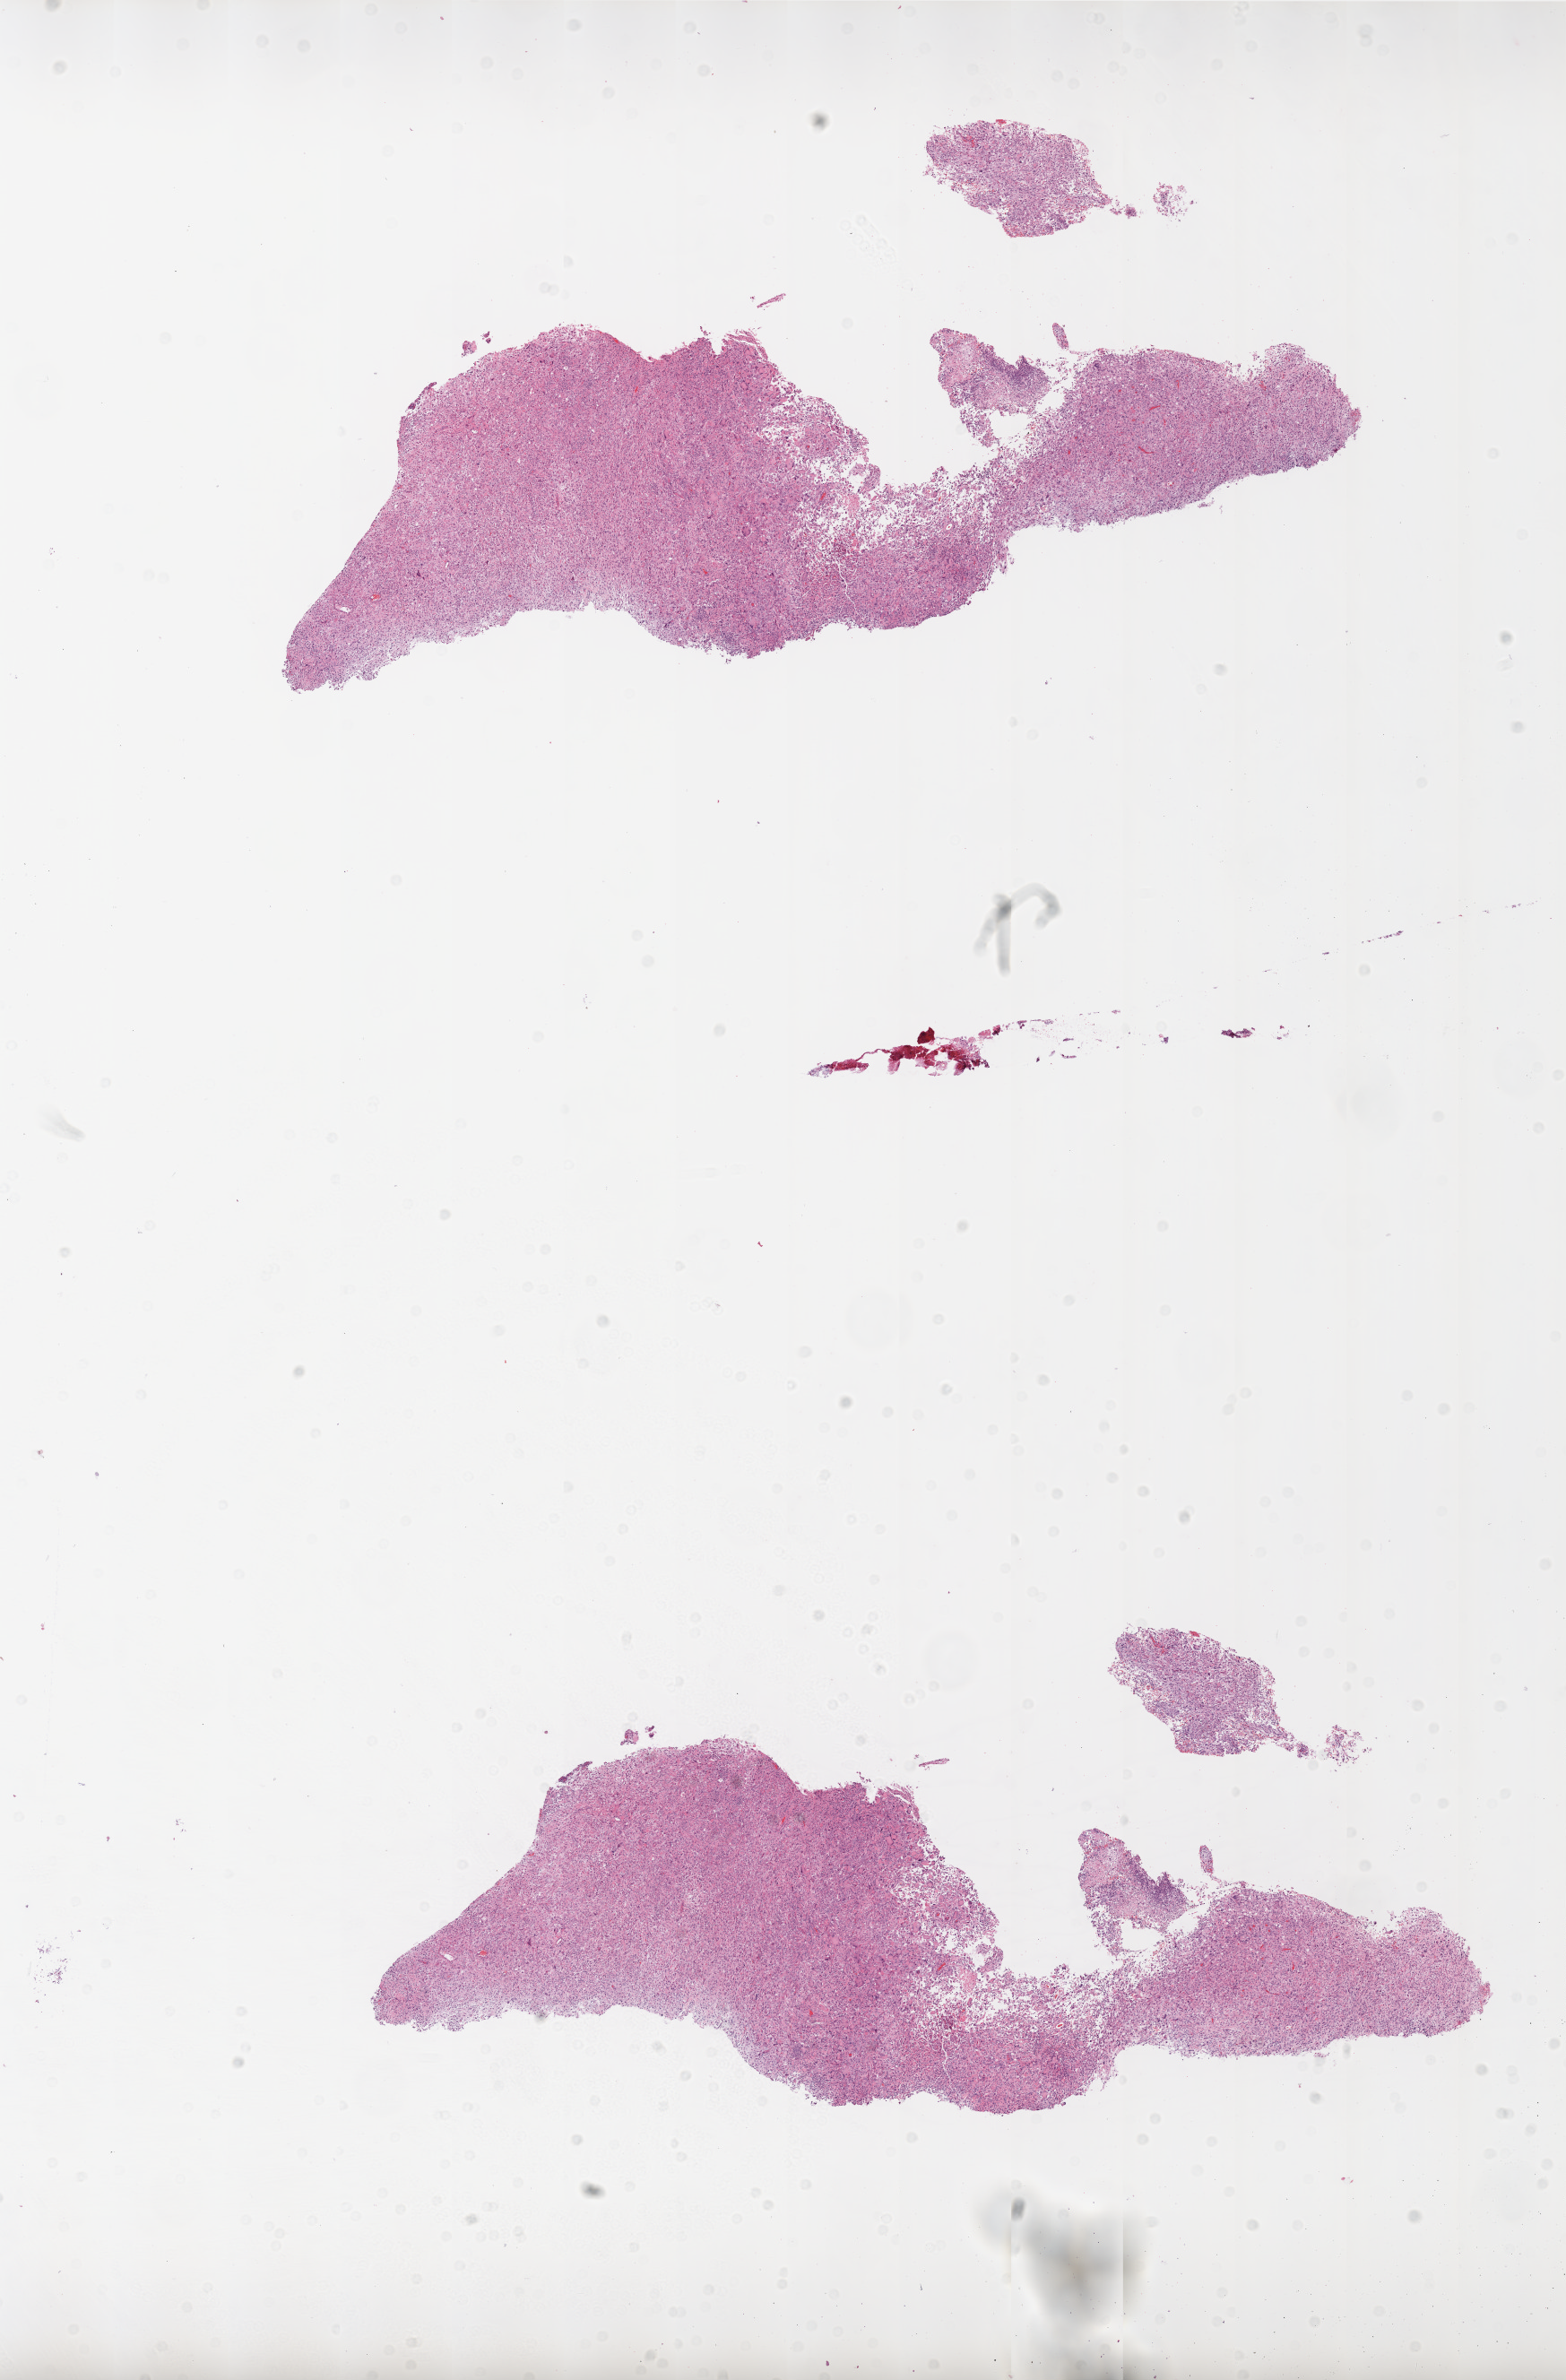
H&E-stained whole-slide image — whole scanned area (about 14.0 x 21.3 mm, acquisition: 20x scan) shown as a low-resolution overview. FFPE section. Brain, primary tumour sample. Female, age 65 years at initial diagnosis.
Pathologic diagnosis: Glioblastoma.